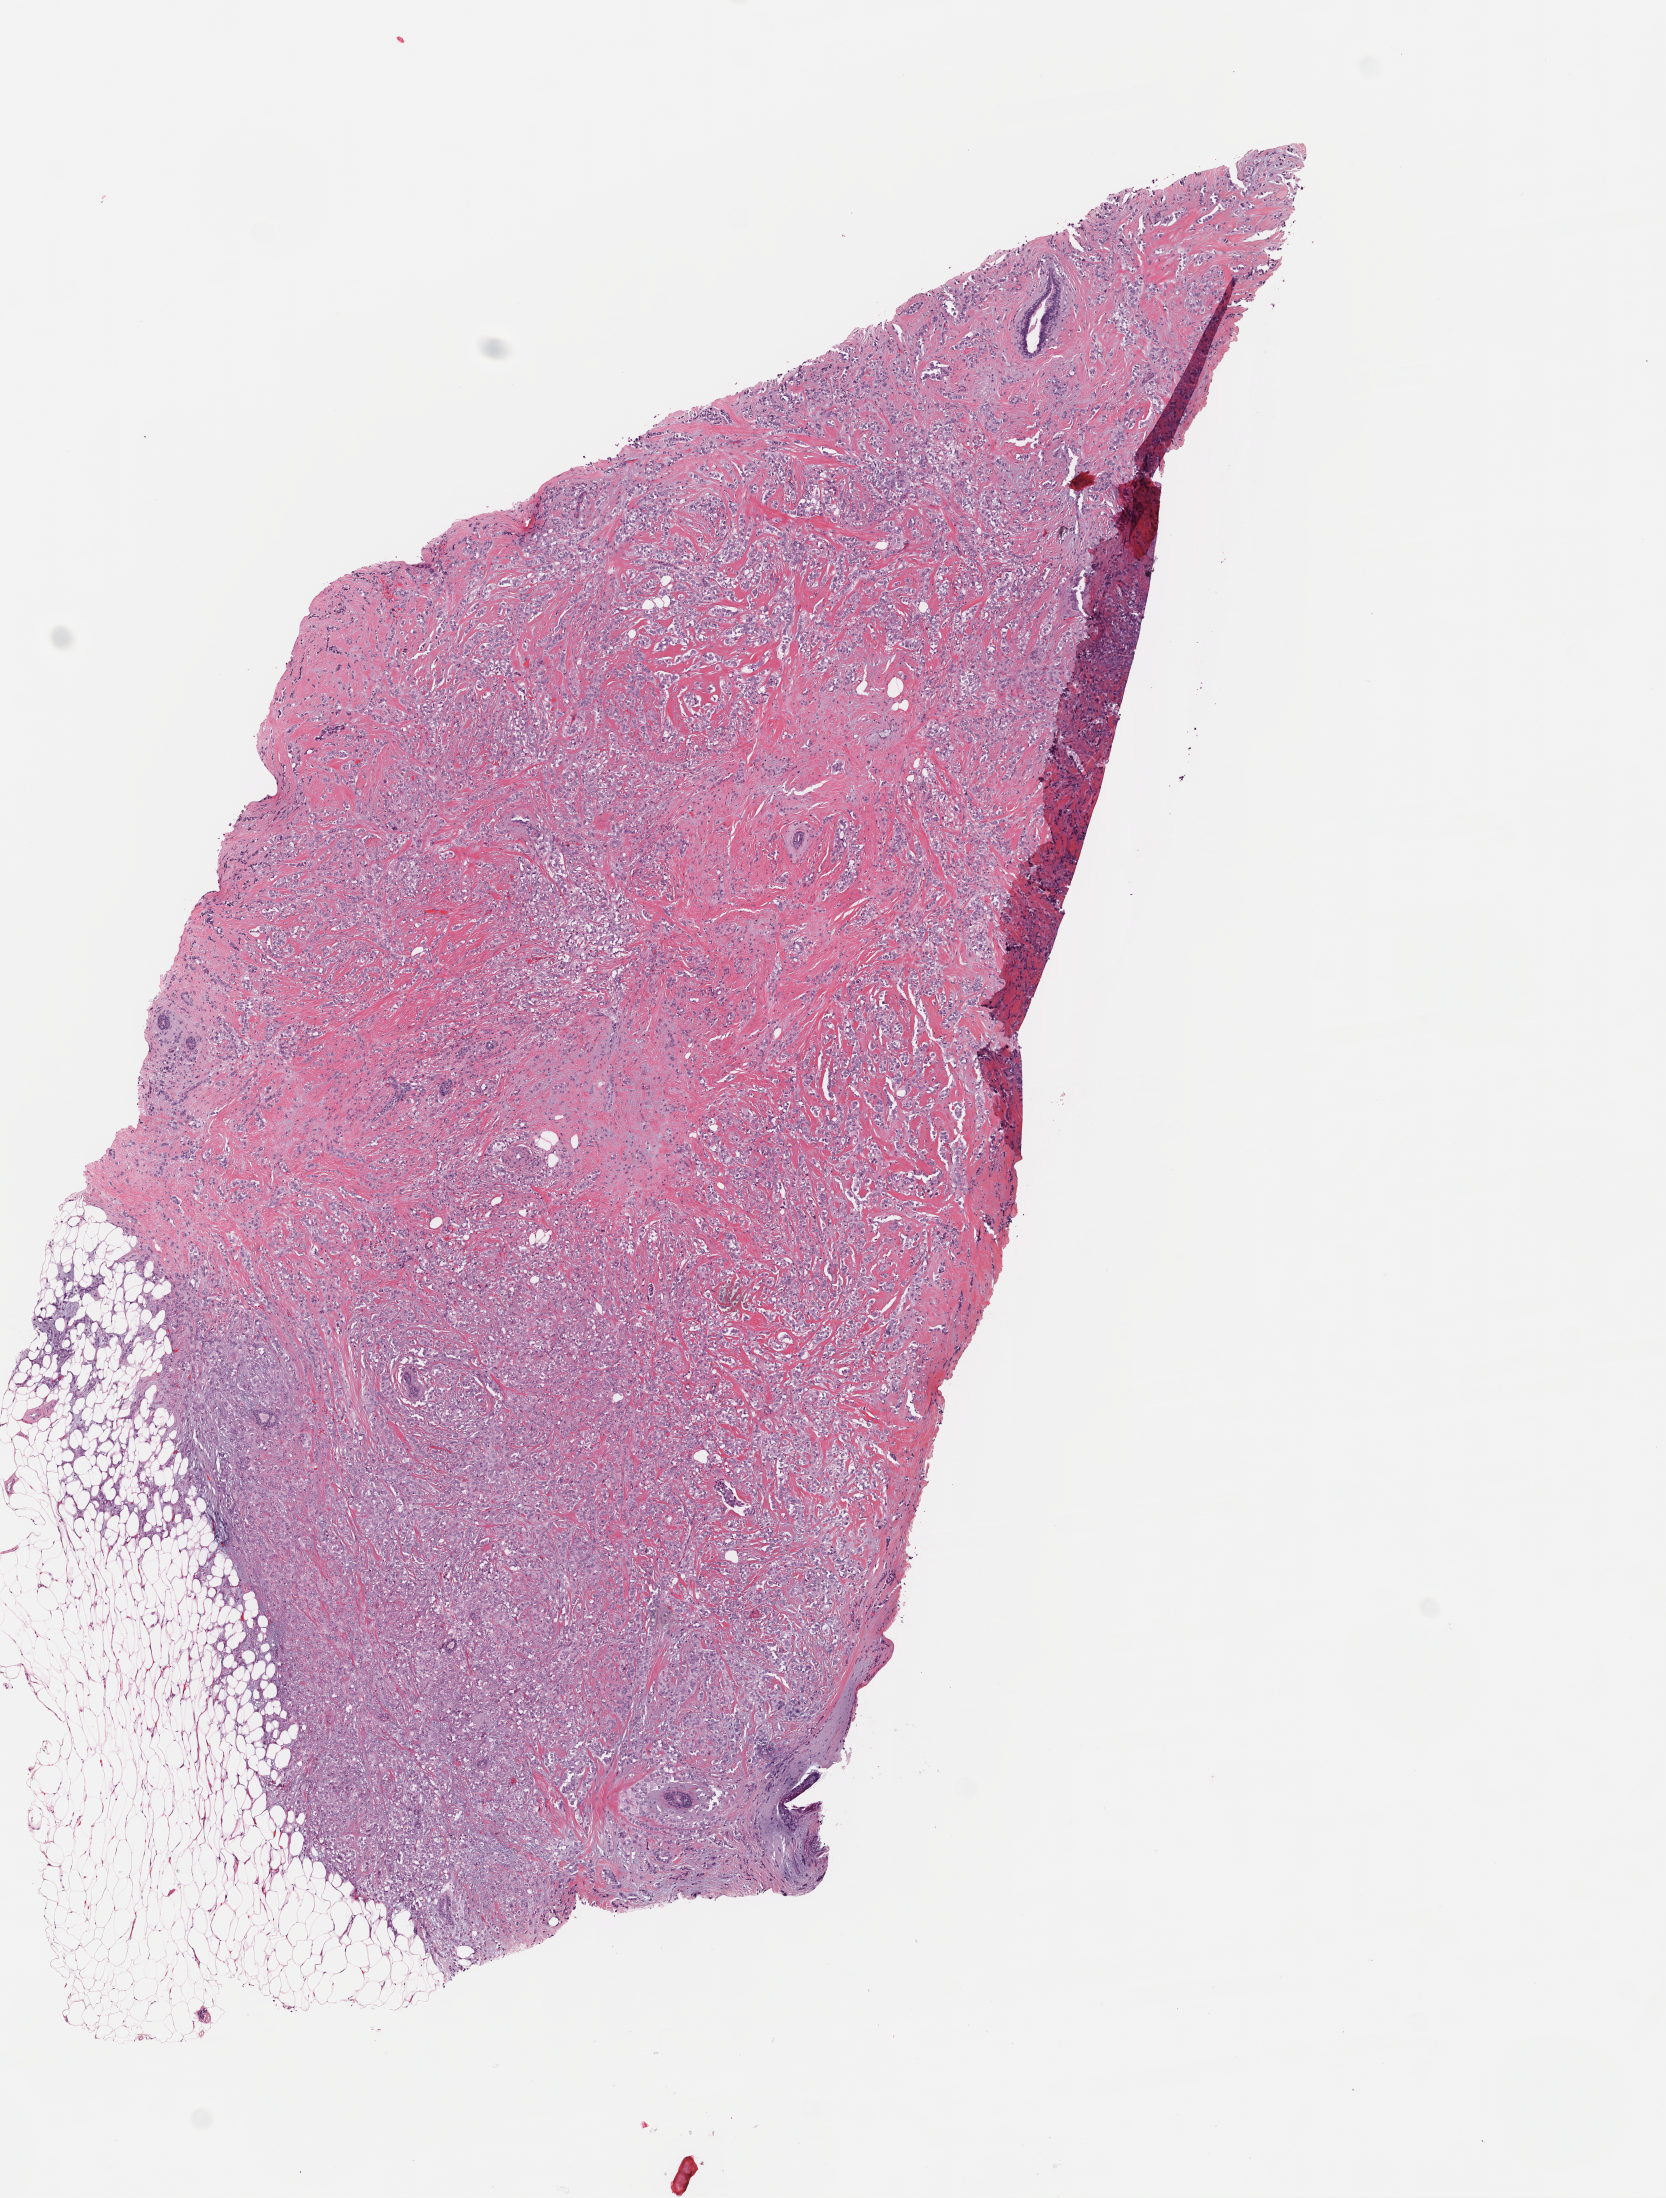
H&E whole-slide image — whole scanned area (about 6.5 x 8.6 mm, from a 40x scan) shown as a low-resolution overview. Frozen section. Sample: primary tumour, breast. Patient: female, age at initial diagnosis 71 years. Composition of this section per pathologist review: tumour cells 79%, tumour nuclei 80%, normal cells 1%, stromal cells 20%, necrosis 0%. Infiltration values recorded for this section: lymphocyte infiltration 2%, monocyte infiltration 0%, neutrophil infiltration 0%.
AJCC pathologic stage: IIIA (7th edition). Pathologic diagnosis: Lobular carcinoma, NOS. Laterality: left. Lymph nodes positive (case pathology): 0 of 16 examined.